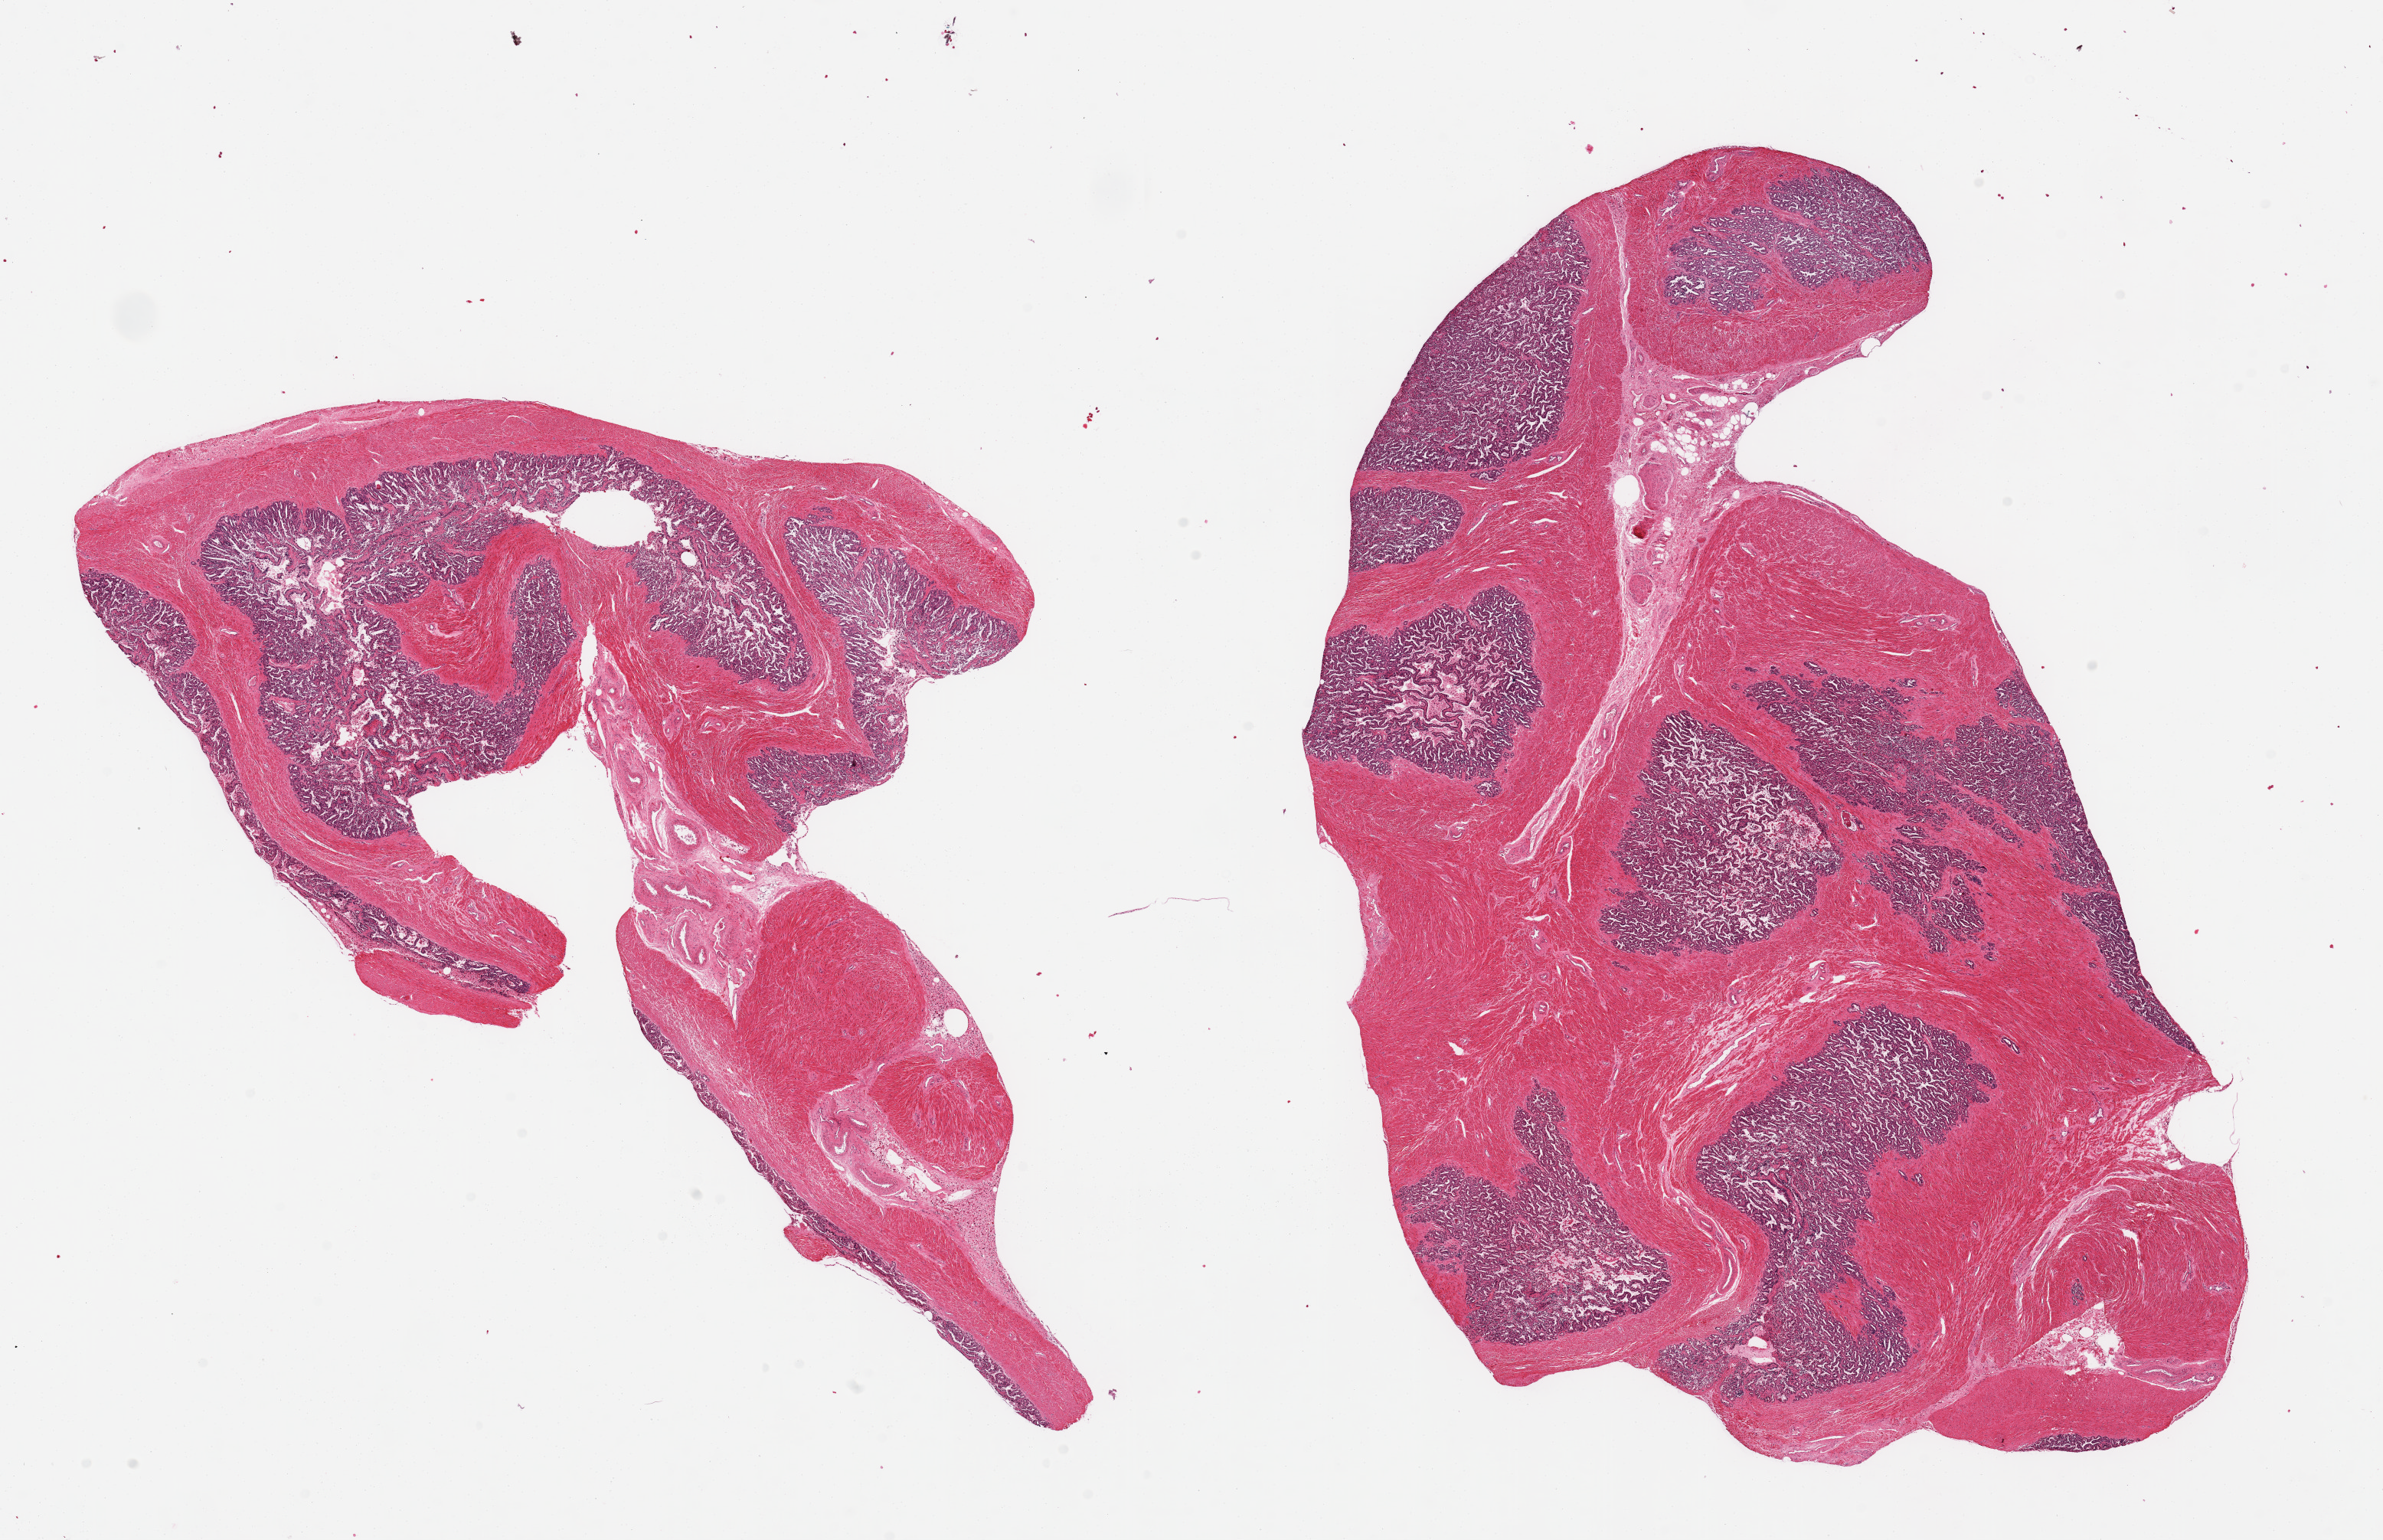
H&E whole-slide image — low-resolution overview of the scanned area, about 24.6 x 15.9 mm; PAXgene-fixed, paraffin-embedded tissue; sampled site (target tissue): prostate; tissue donor sample. Donor sex: male.
Reviewer comment on this tissue sample: 2 pieces. Not target prostate; seminal vesicle.